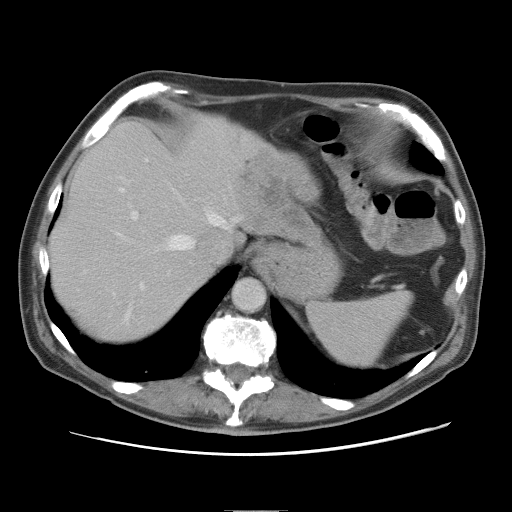
Contrast-enhanced abdominal CT, one axial slice. Position 63 of 89 along the scan axis. 120 kVp. Intravenous contrast given. Soft-tissue window (W 400 / L 40 HU). 5 mm slice thickness. 512 × 512 image matrix. Male patient, age 69 years. From the clinical record (not read from this slice): diagnosis: colorectal cancer liver metastases, imaged before liver resection; multiple liver metastases: no; largest metastasis: 8.5 cm.
Structures marked on this image (expert manual segmentation):
- hepatic veins: bounding box <117,187,239,320> (left, top, right, bottom; pixels)
- liver: <52,117,312,342>
- planned liver remnant (the part of the liver to remain after resection): <51,117,244,342>
- portal vein (with intrahepatic branches): <131,159,148,220>
- liver metastasis: <239,152,304,230>